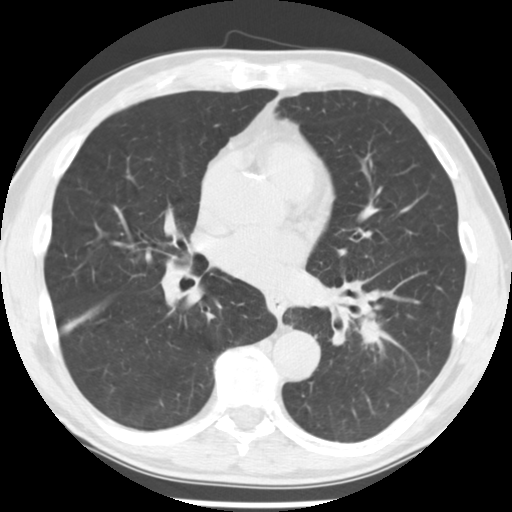
Low-dose screening chest CT, axial slice; third annual screen; lung window (W 1500 / L -600 HU); 2.5 mm slice thickness; standard (soft-tissue) reconstruction kernel (STANDARD); 120 kVp; slice 114 of 242 in the series; 512 × 512 image matrix. Male, age 64 years at enrolment. Current smoker at enrolment.
Expert-annotated lung lesion, bounding box [x1, y1, x2, y2] px = [351, 318, 389, 349]. No non-calcified nodule or mass ≥4 mm was recorded by the screening reader at this exam. Lung cancer was diagnosed 203 days after this screen: adenocarcinoma, NOS, left lower lobe, stage IV (AJCC 6th edition), 44 mm at pathology.